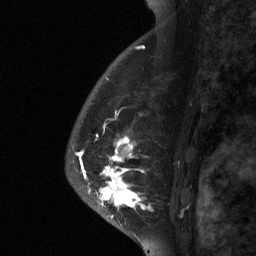
Breast MRI (dynamic contrast-enhanced), one sagittal slice. Position 47 of 64 along the scan axis. Dynamic contrast-enhanced study with each time point stored as its own series, time point 2 of 3 at this slice position (early post-contrast, ordered by acquisition time). 1.5 T. TE 4.8 ms, TR 27 ms. 2 mm slice thickness. 256 × 256 image matrix, field of view 180 × 180 mm. Female patient, age 56 years. Case-level facts recorded for this patient, not image findings: setting: breast cancer imaged before/during neoadjuvant chemotherapy; receptor status: HER2-positive.
Structures marked on this image (semi-automatic segmentation, software-assisted and operator-edited):
- analysis volume of interest (the breast-tissue region the enhancement analysis was run in; not a lesion): bounding box [x1, y1, x2, y2] px = [87, 104, 182, 229]
- tumour enhancement mask (voxels above the 90 % enhancement threshold inside the analysis volume of interest): [88, 137, 153, 211]